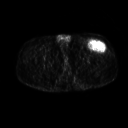
FDG PET of an extremity soft-tissue mass (from a PET/CT study), one axial slice. Position 251 of 267 along the scan axis. 3.27 mm slice thickness. 128 × 128 image matrix. Patient: male, 64 years. From the clinical record (not read from this slice): histological type: extraskeletal osteosarcoma; grade: high; site of the primary tumour: thigh.
Outlined on this slice (expert contour drawn on MRI and transferred to this co-registered scan by the dataset authors):
- gross tumour volume (mass): bounding box [x1, y1, x2, y2] px = [89, 42, 106, 51]